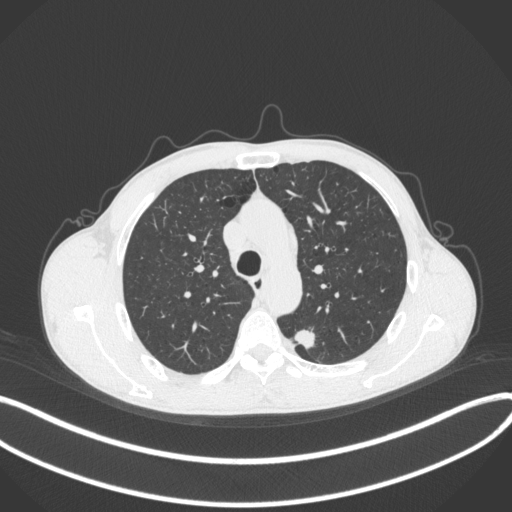
Chest CT, one axial slice. Slice 284 of 429 in the series (ordered by position). 120 kVp. Lung window (W 1500 / L -600 HU). 1 mm slice thickness. 512 × 512 image matrix. Patient: male, 51 years. Case-level facts recorded for this patient, not image findings: clinical TNM (as recorded): T2a N1 M1.
Structures marked on this image (bounding box drawn by a radiologist):
- lung tumour (recorded histology: adenocarcinoma): bounding box [x1, y1, x2, y2] px = [290, 321, 321, 352]